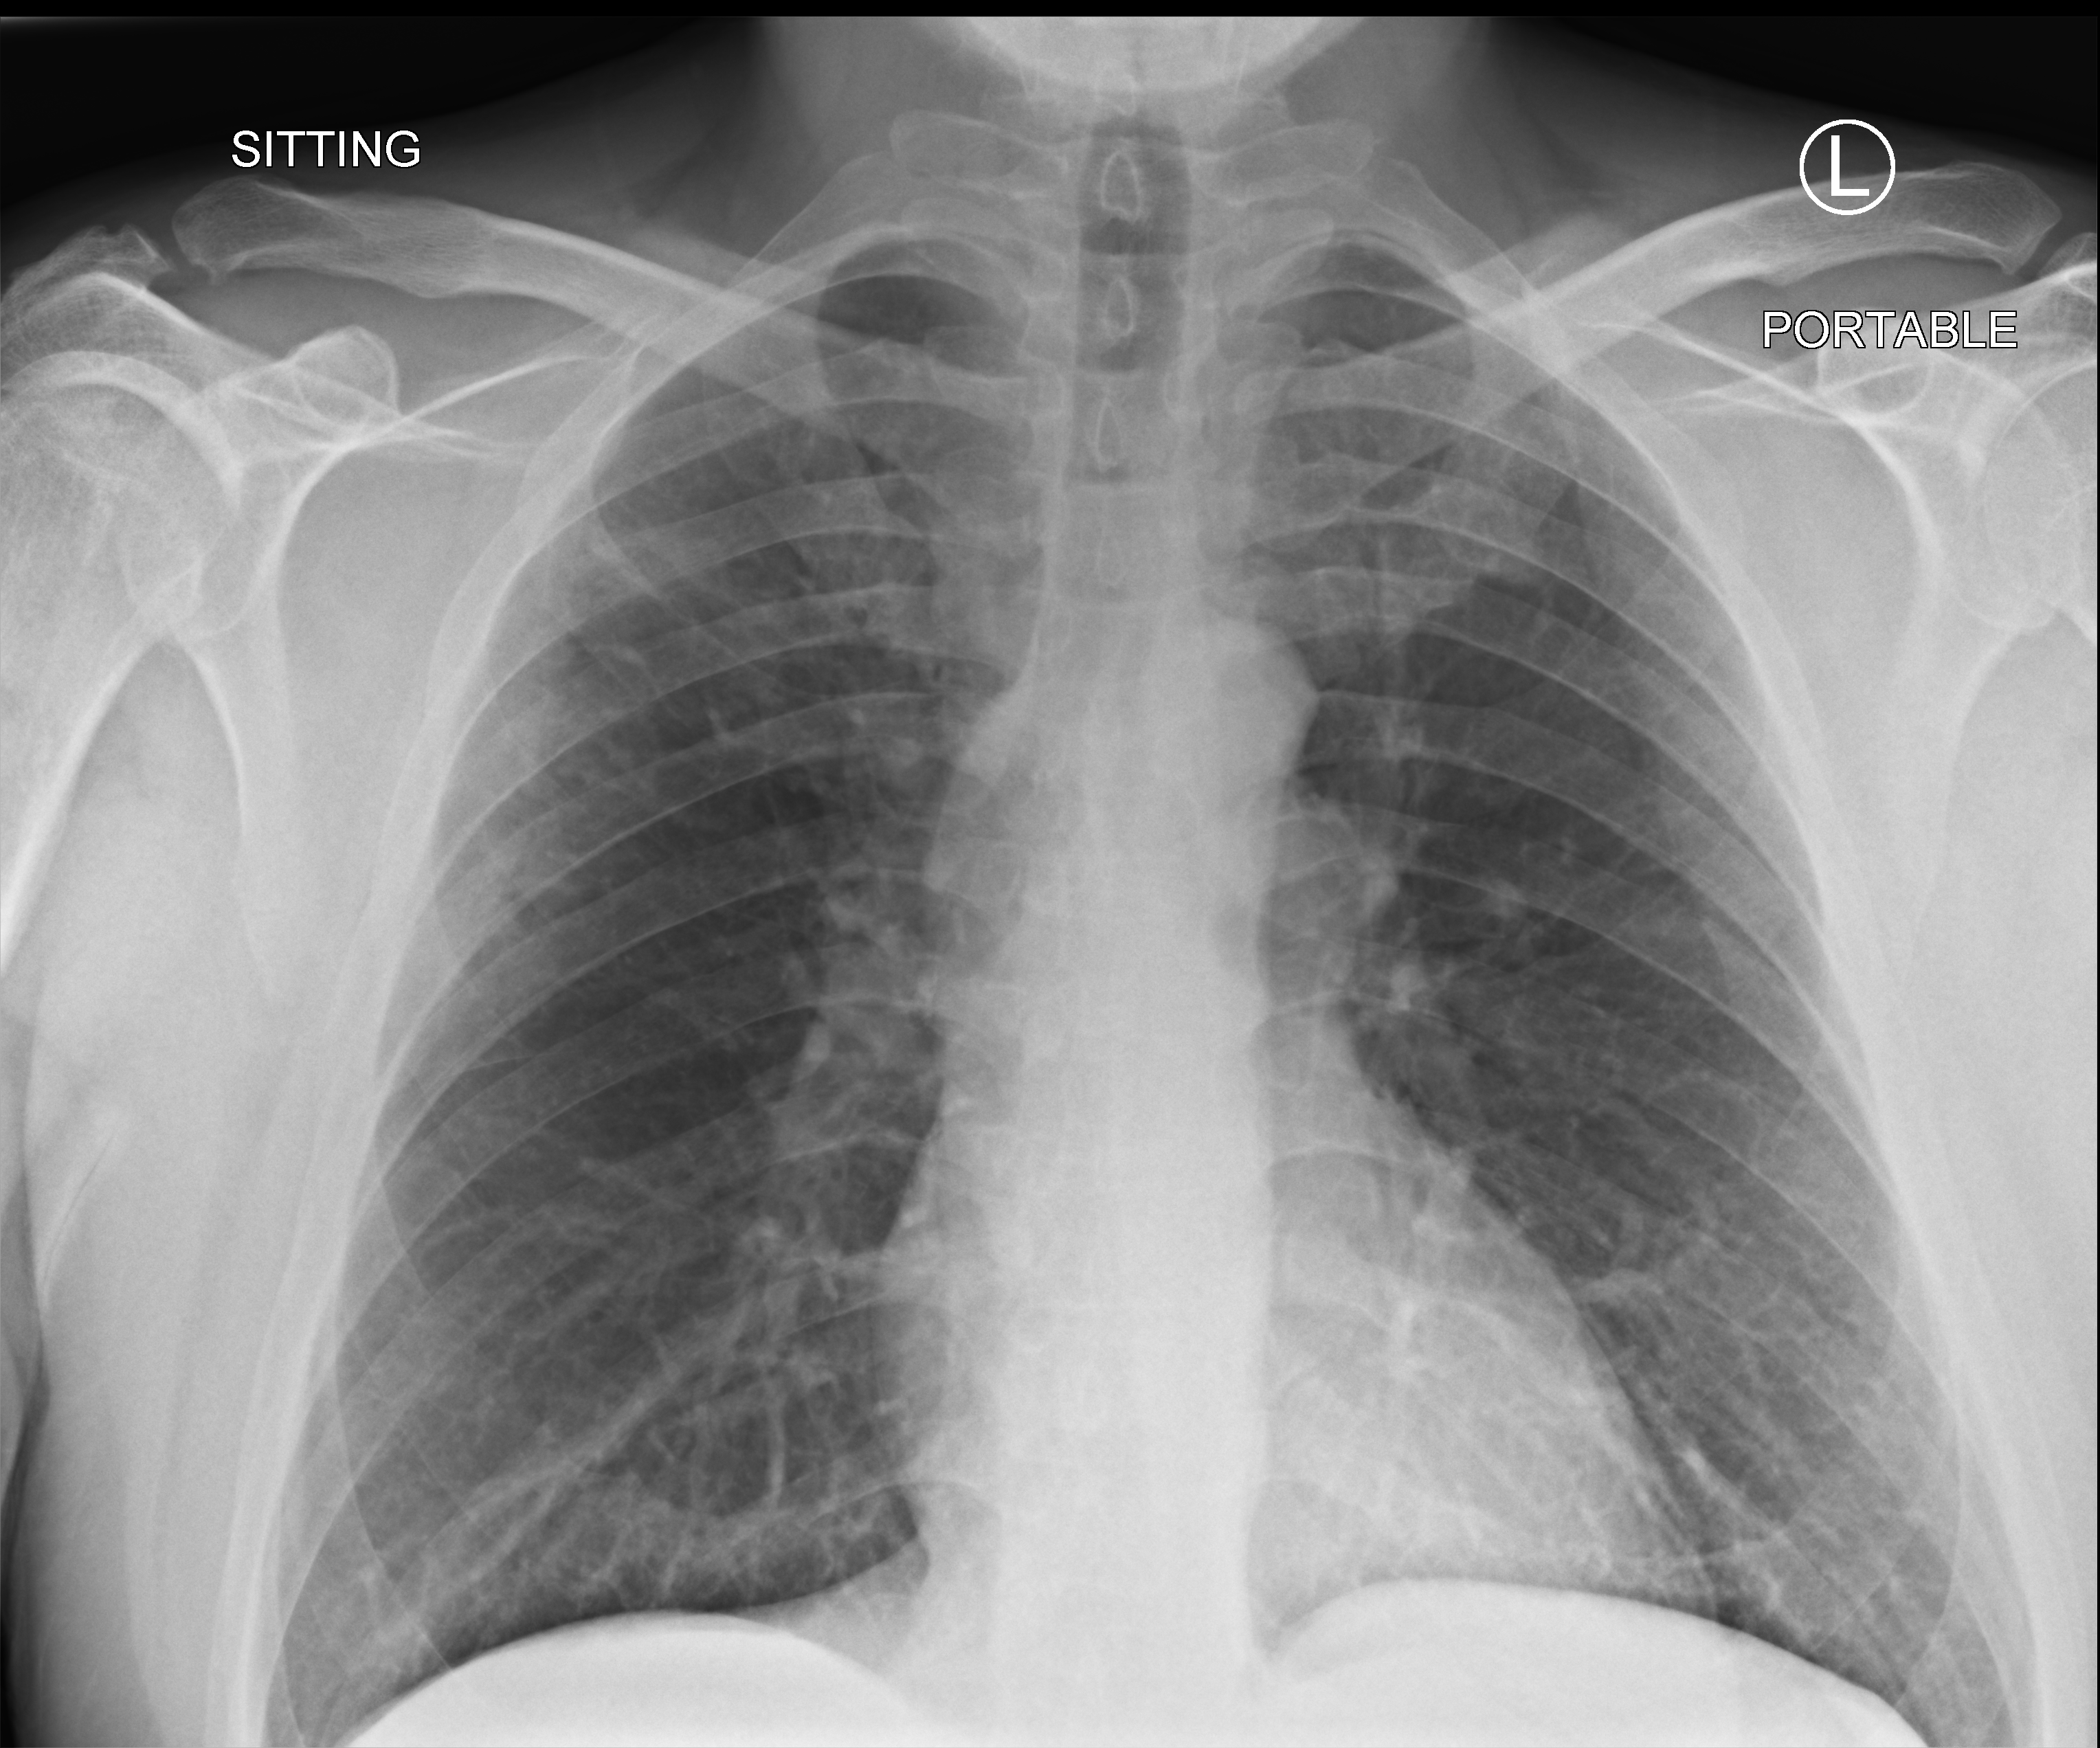
Chest X-ray (portable). Patient hospitalised with COVID-19; male, aged 18–59 years.
Admission-level facts for this patient (not findings on this image; timing relative to this image not recorded):
- mechanically ventilated during this hospital stay: no
- admitted to intensive care during this hospital stay: no